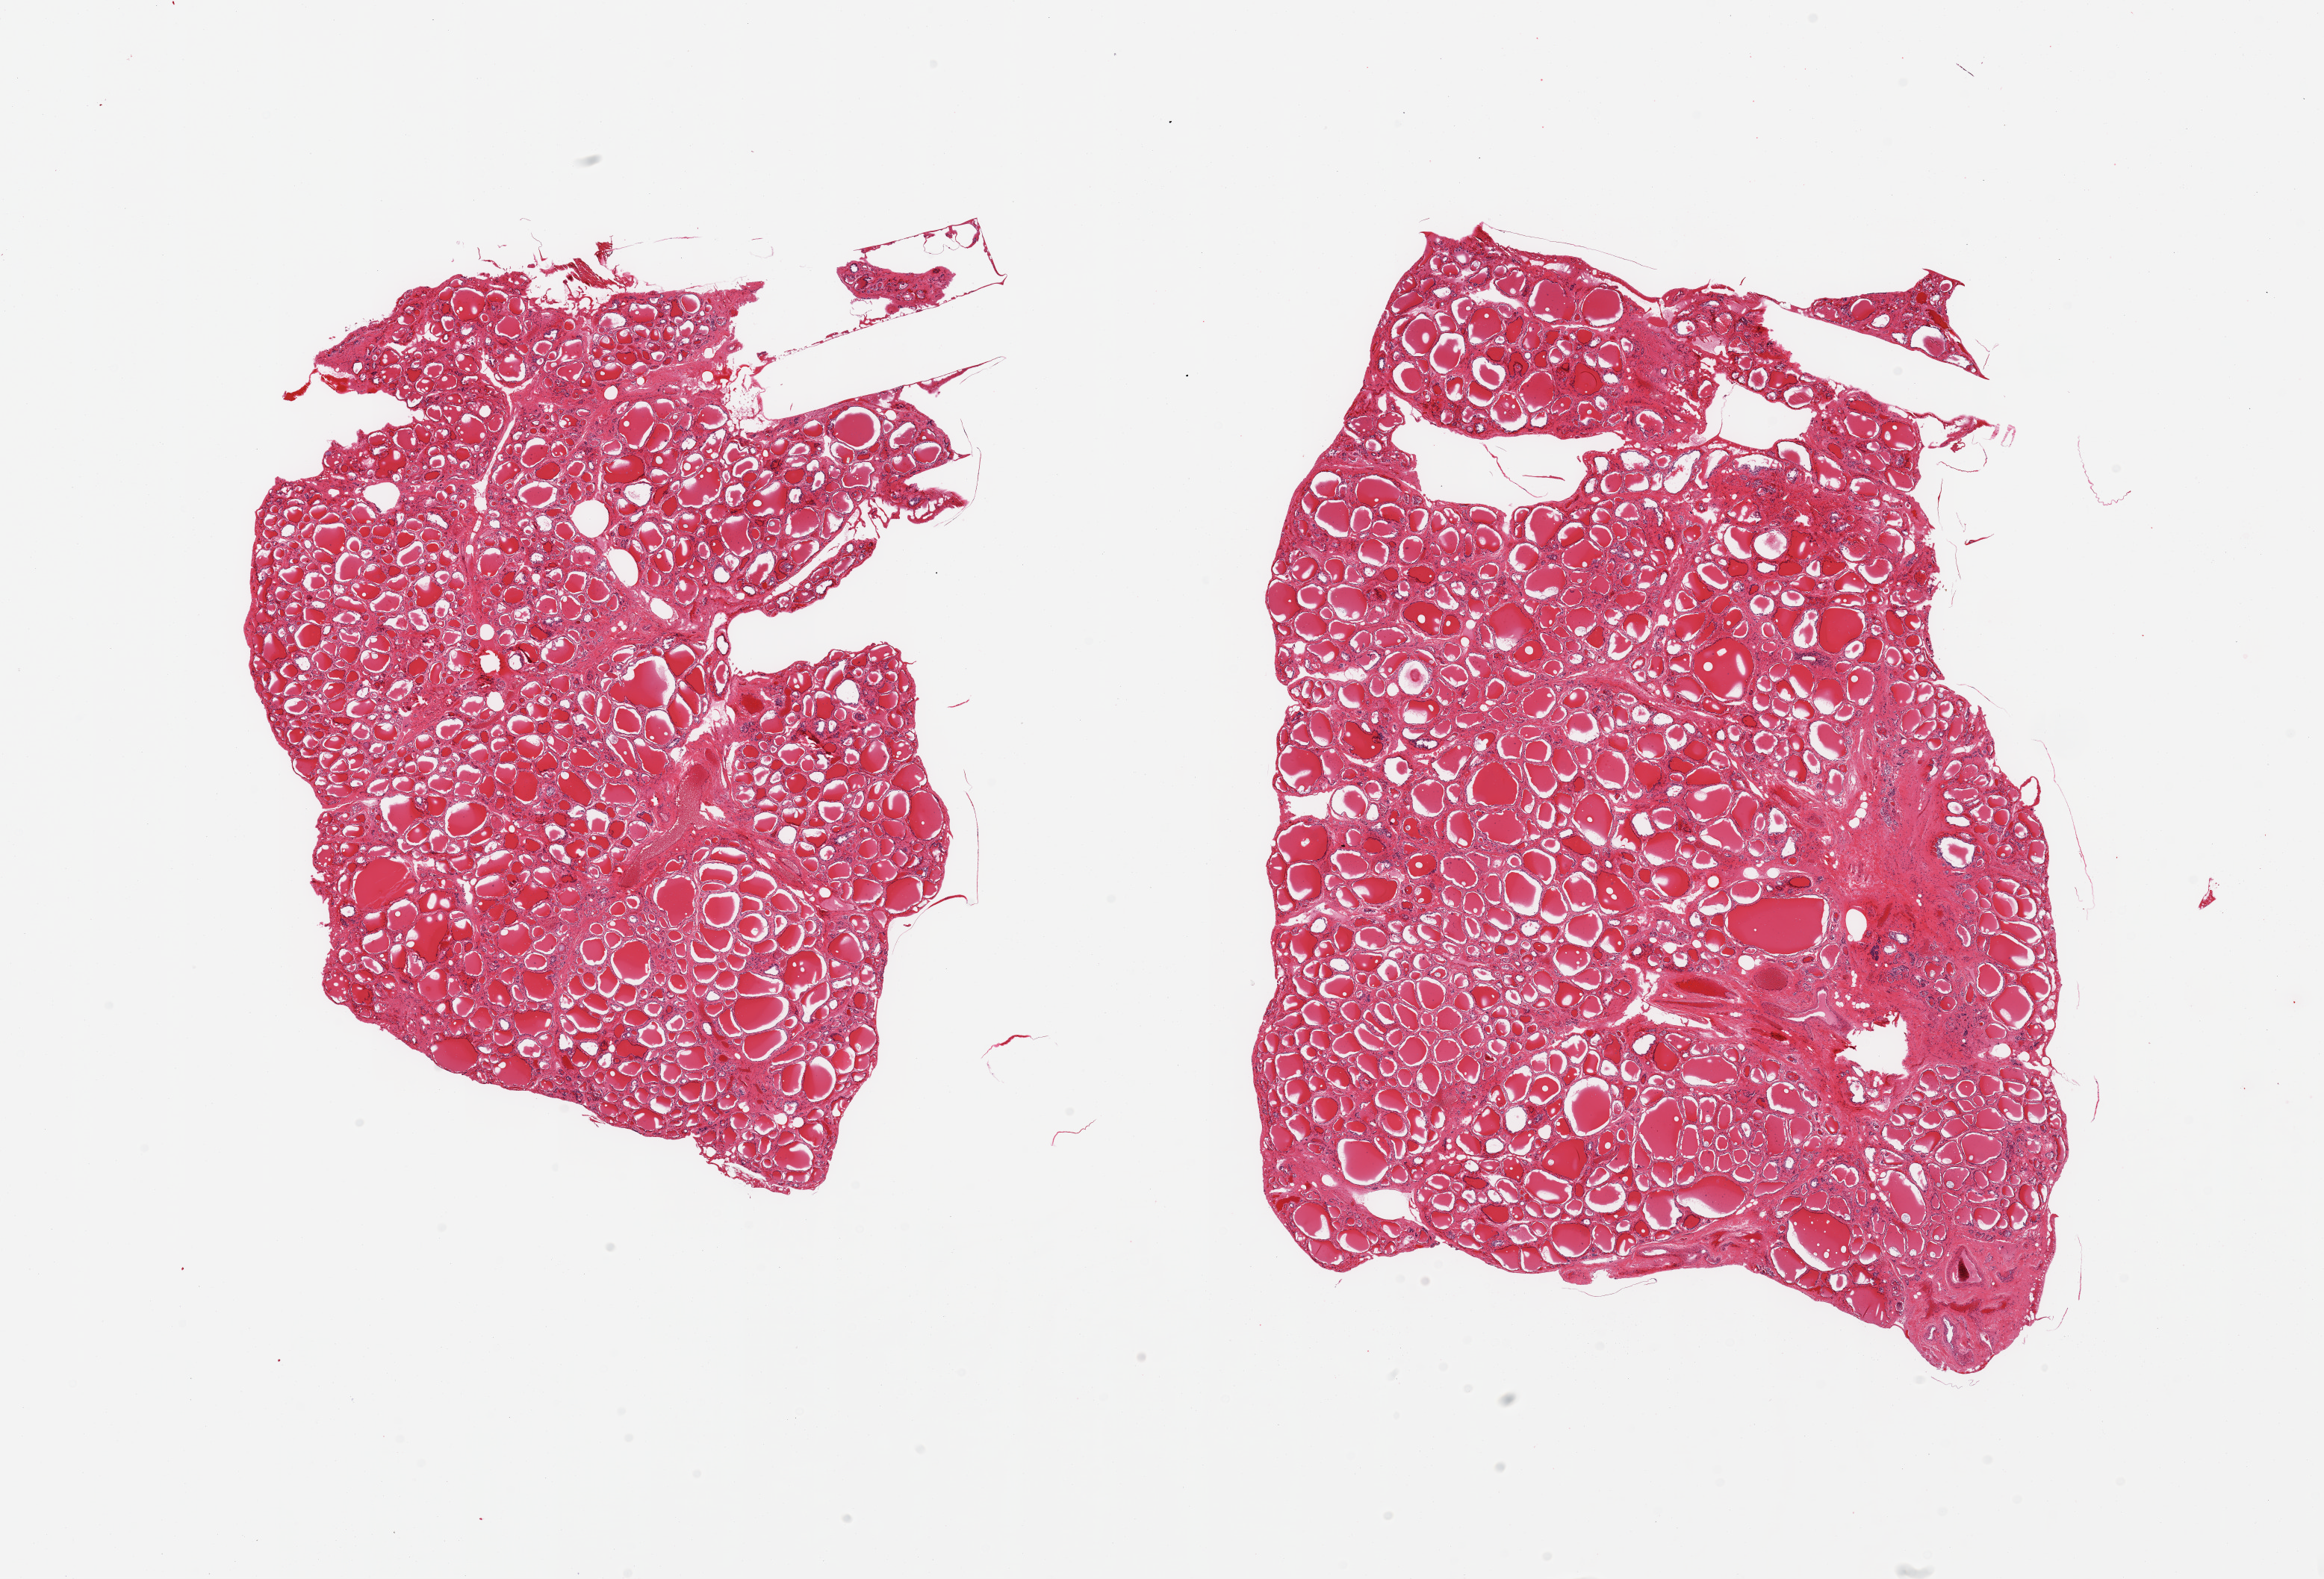
Digitized hematoxylin and eosin (H&E)-stained section, whole scanned area (about 24.6 x 16.7 mm) shown as a low-resolution overview. PAXgene-fixed paraffin-embedded (PFPE) section. Section of thyroid (target tissue). Donor tissue sample. Donor sex: male.
Pathologist's review note for this sample: 2 pieces; interstitial fibrosis with discrete nodularity.